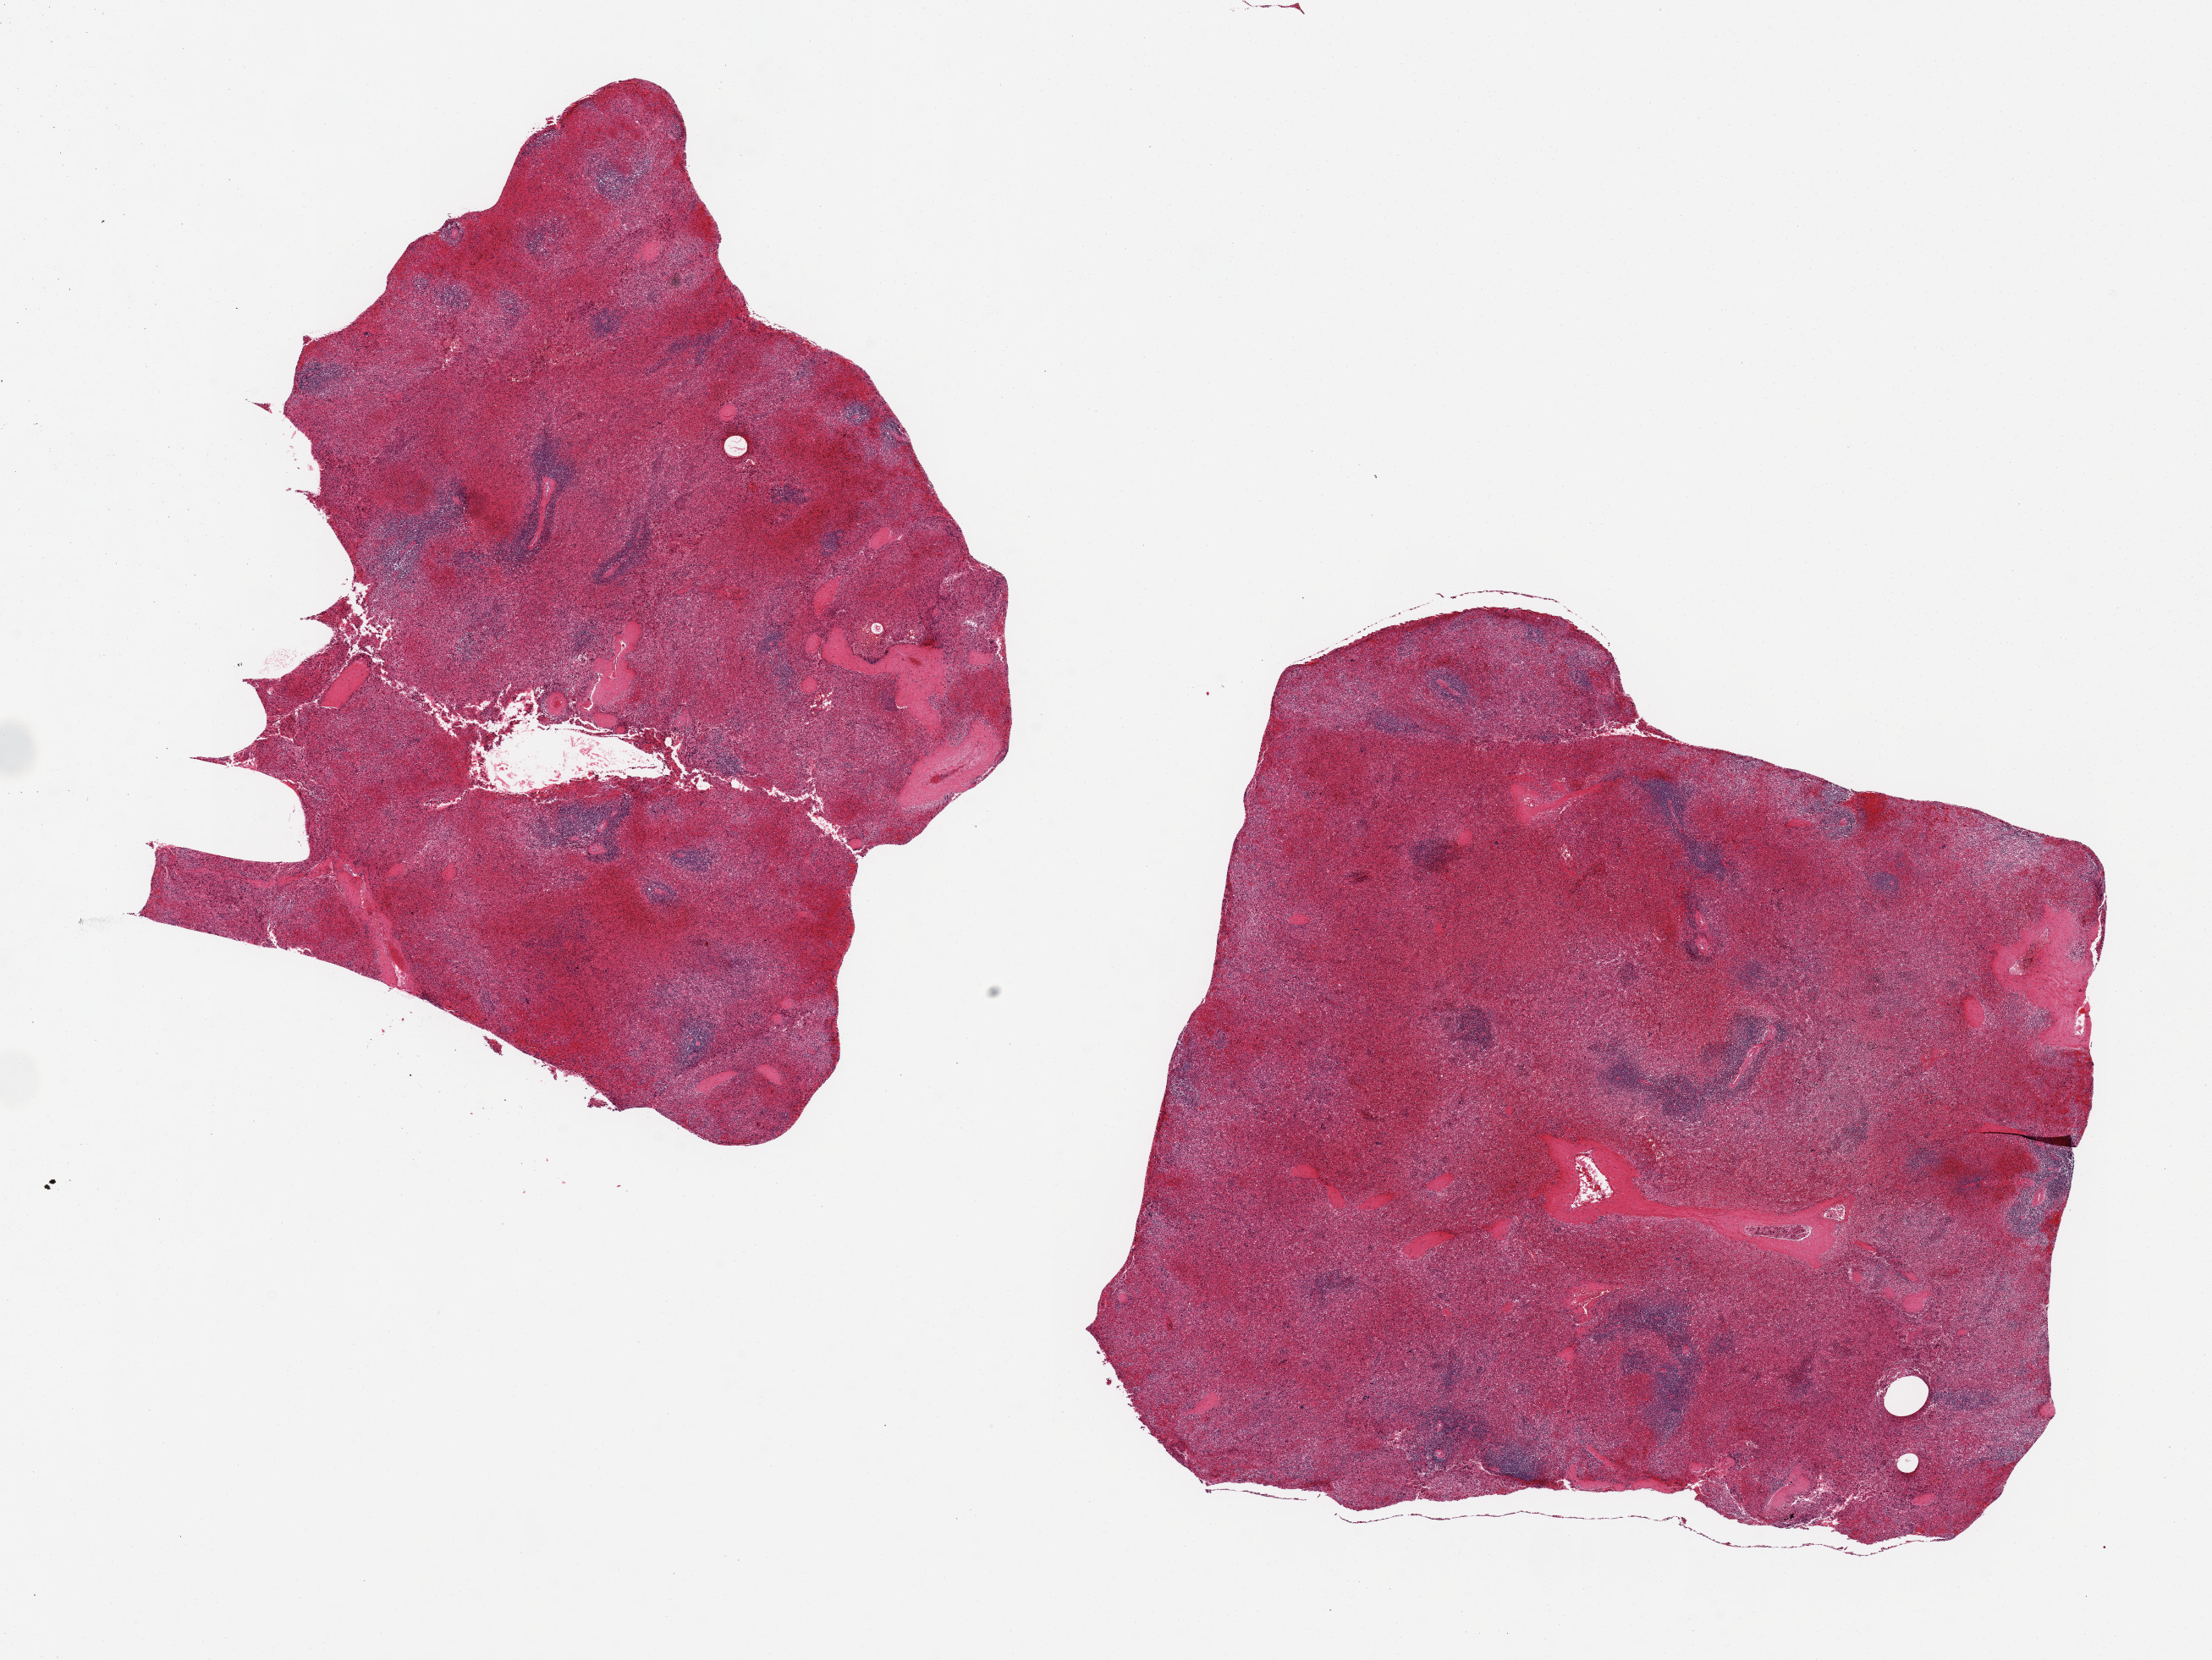
Digitized H&E-stained section, brightfield — low-resolution overview of the scanned area, about 20.7 x 15.5 mm (acquisition: 20x scan); PAXgene-fixed, paraffin-embedded tissue; target tissue: spleen; donor tissue sample.
Review note (as recorded): 2 ~9x8mm aliquots.